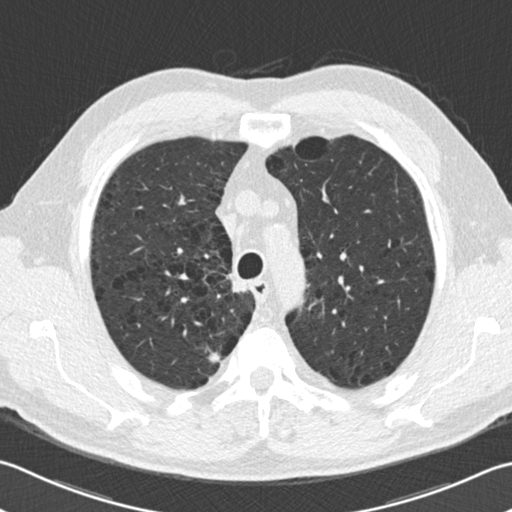
Chest CT (low-dose screening protocol), one axial image. Second screening round (one year after baseline). Lung window (W 1500 / L -600 HU). Standard (soft-tissue) reconstruction kernel (B30f). 120 kVp. Slice 48 of 206 in the series. 512 × 512 image matrix, field of view 346 × 346 mm. Male participant, aged 68 years at enrolment.
• Expert reader's lesion annotation, box from (x=197, y=341) to (x=229, y=372) px.
• The exam's reader record, not a measurement of the box and not confirmed to be the same lesion: non-calcified nodule or mass ≥4 mm, right upper lobe, 30 × 20 mm, smooth margins, pre-existing on the prior screen: no.
• Official screen result: positive, change unspecified: nodule(s) >= 4 mm or enlarging nodule(s), mass(es), or other non-specific abnormalities suspicious for lung cancer.
• Later outcome: lung cancer diagnosed 414 days after this screen — adenocarcinoma, NOS, right upper lobe, well differentiated (G1), stage IB (AJCC 6th edition), 15 mm at pathology.